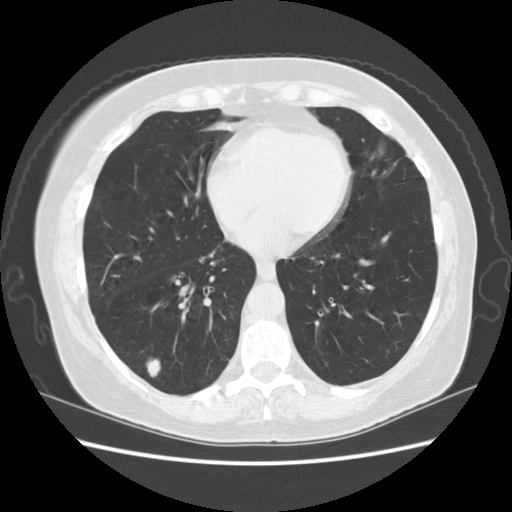
Axial slice from a low-dose chest CT screening exam; third annual screen; lung window (W 1500 / L -600 HU); 512 × 512 image matrix. Female participant, aged 59 years at enrolment.
Expert-annotated lung lesion, bounding box [x1, y1, x2, y2] px = [133, 351, 172, 387]. The exam's reader record, not a measurement of the box and not confirmed to be the same lesion: non-calcified nodule or mass ≥4 mm, right lower lobe, 16 × 11 mm, smooth margins, soft tissue attenuation, pre-existing on the prior screen: yes; interval growth: yes. Official screen result: positive, other.